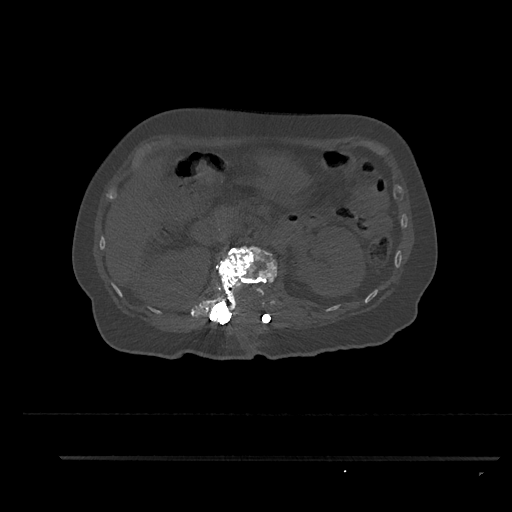
CT including the spine, one axial slice. Position 212 of 797 along the scan axis. Reconstruction kernel Br40s/3. Bone window (W 1800 / L 400 HU). 0.5 mm slice thickness. 512 × 512 image matrix, field of view 408 × 408 mm. Female patient, age 44 years. From the clinical record (not read from this slice): primary cancer: renal; vertebrae with lytic lesions (as recorded): L1.
Structures marked on this image (semi-automatic segmentation, software-assisted and operator-edited):
- L1 vertebra: bounding box <204,246,277,323> (left, top, right, bottom; pixels)